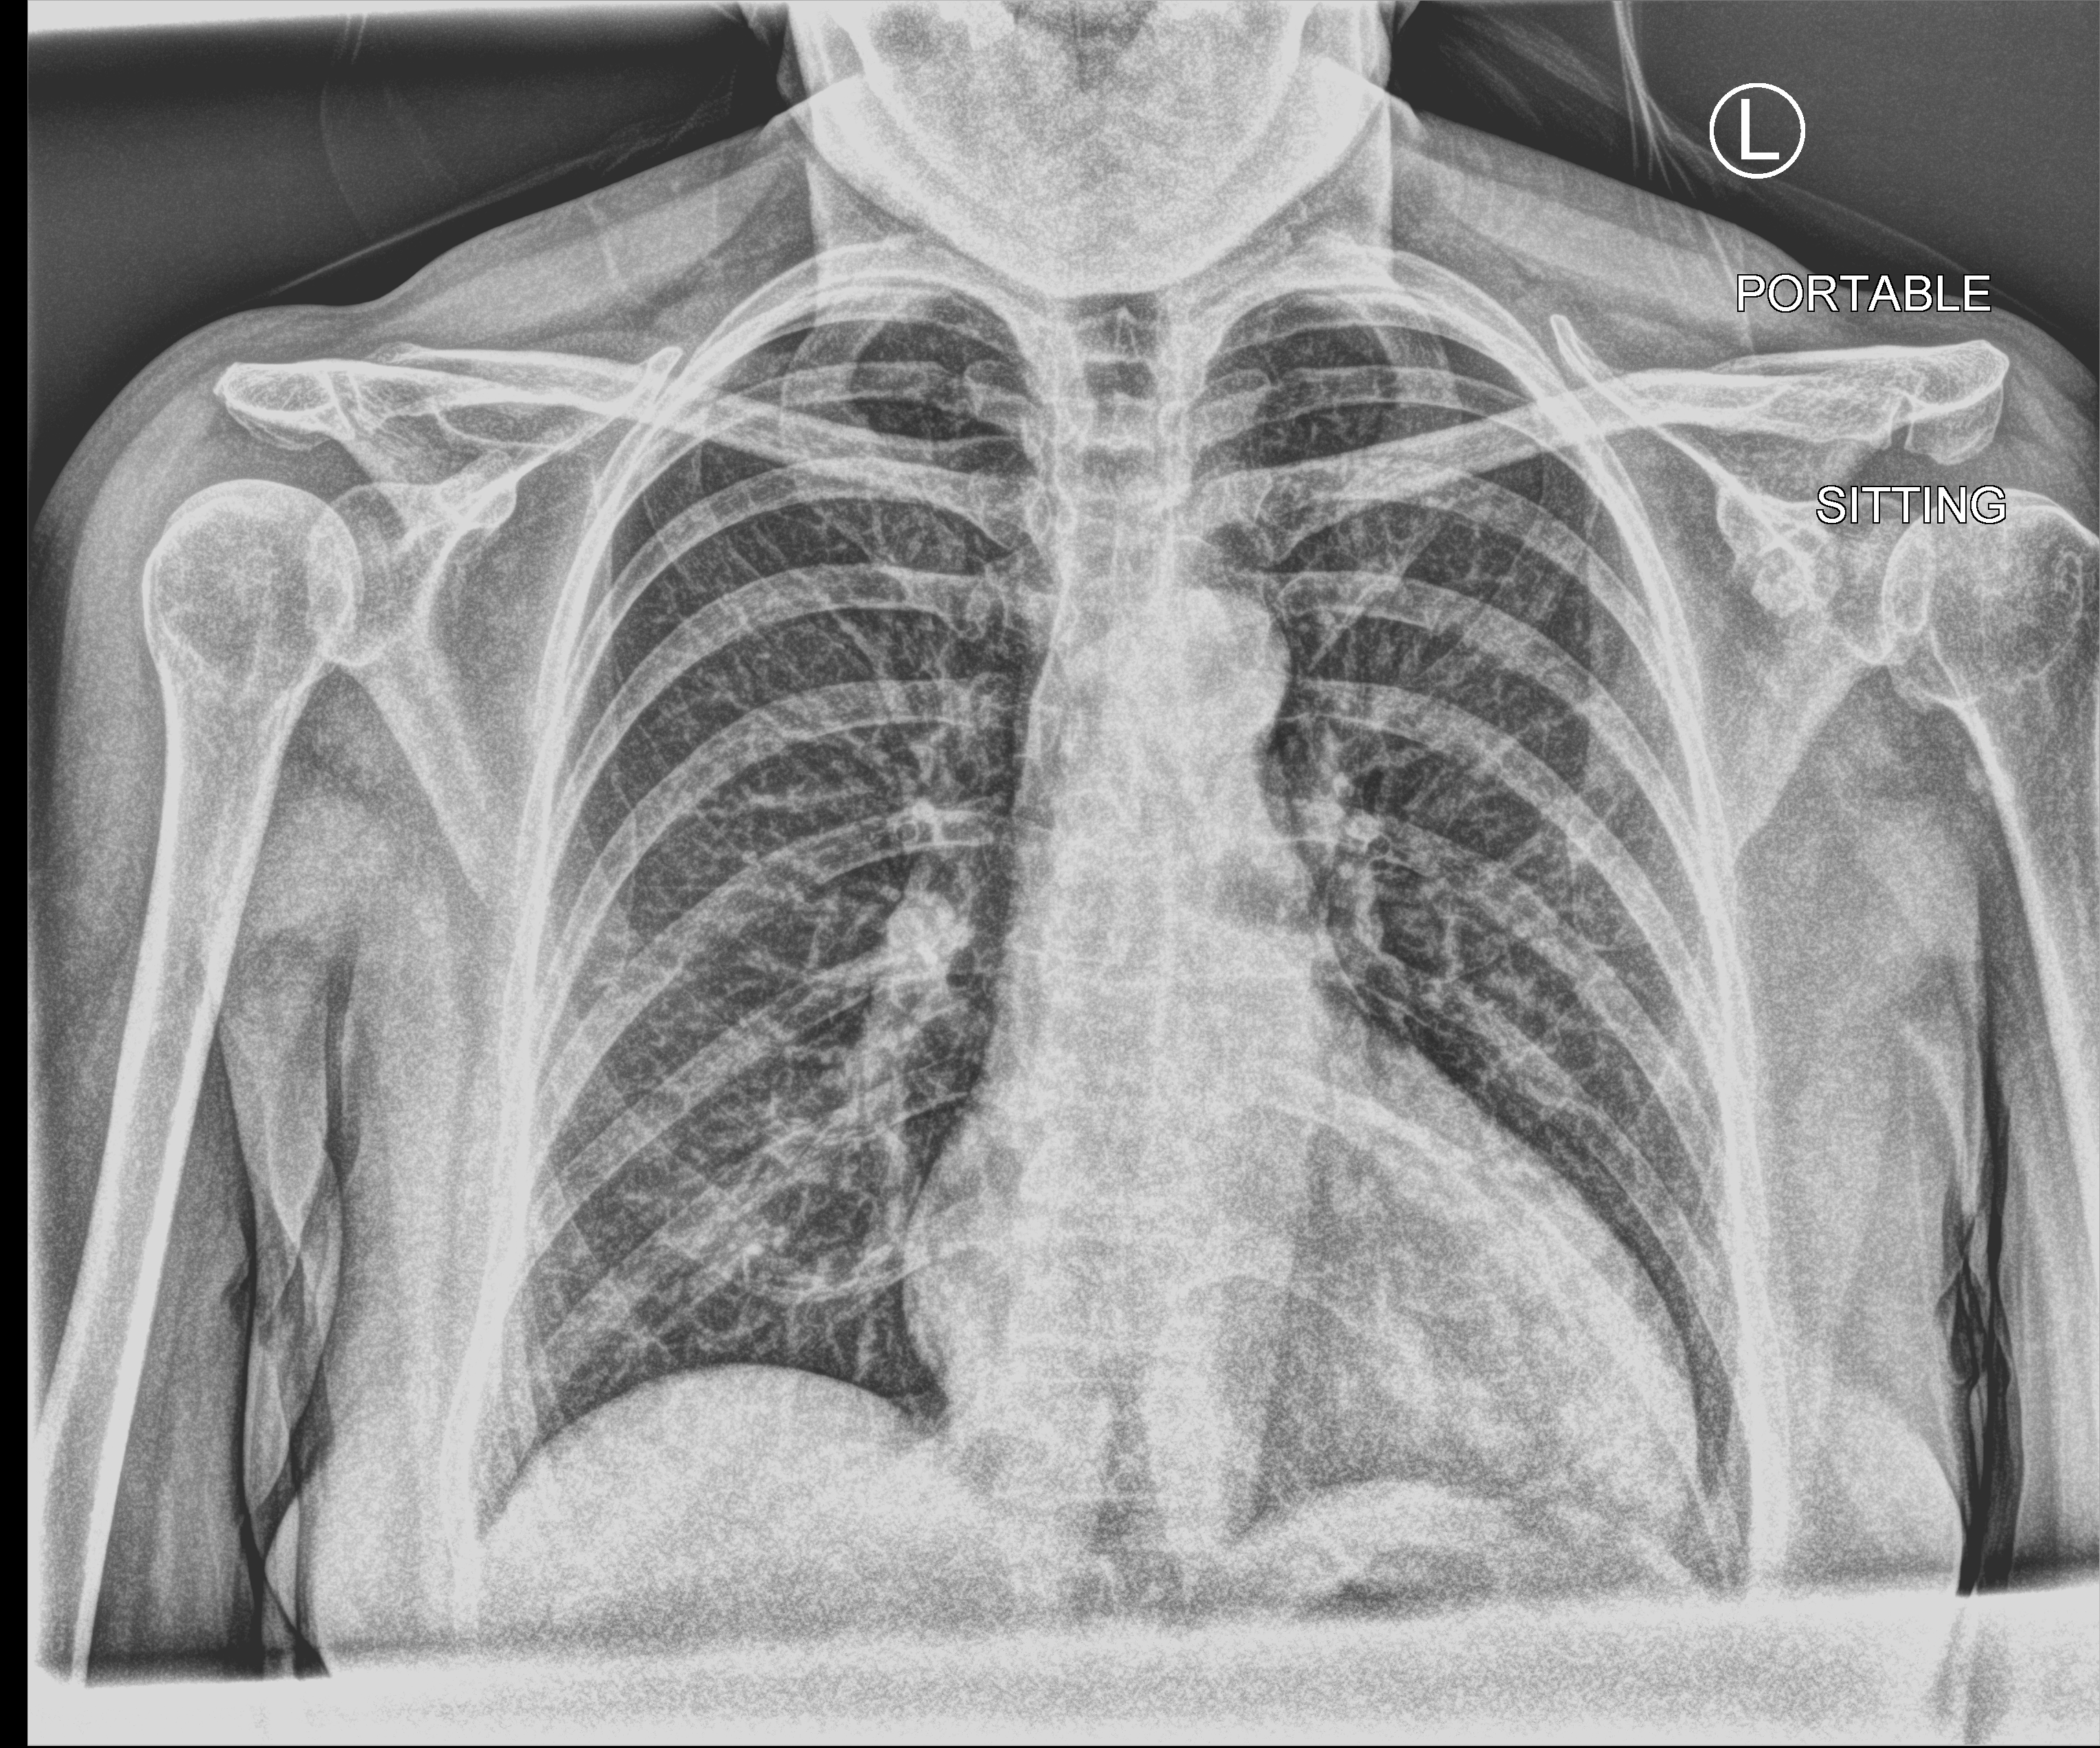
Bedside chest radiograph (computed radiography), anteroposterior (AP) projection. Patient hospitalised with COVID-19; female, aged 60–74 years.
Admission-level facts for this patient (not findings on this image; timing relative to this image not recorded): admitted to intensive care during this hospital stay: no; mechanically ventilated during this hospital stay: no.